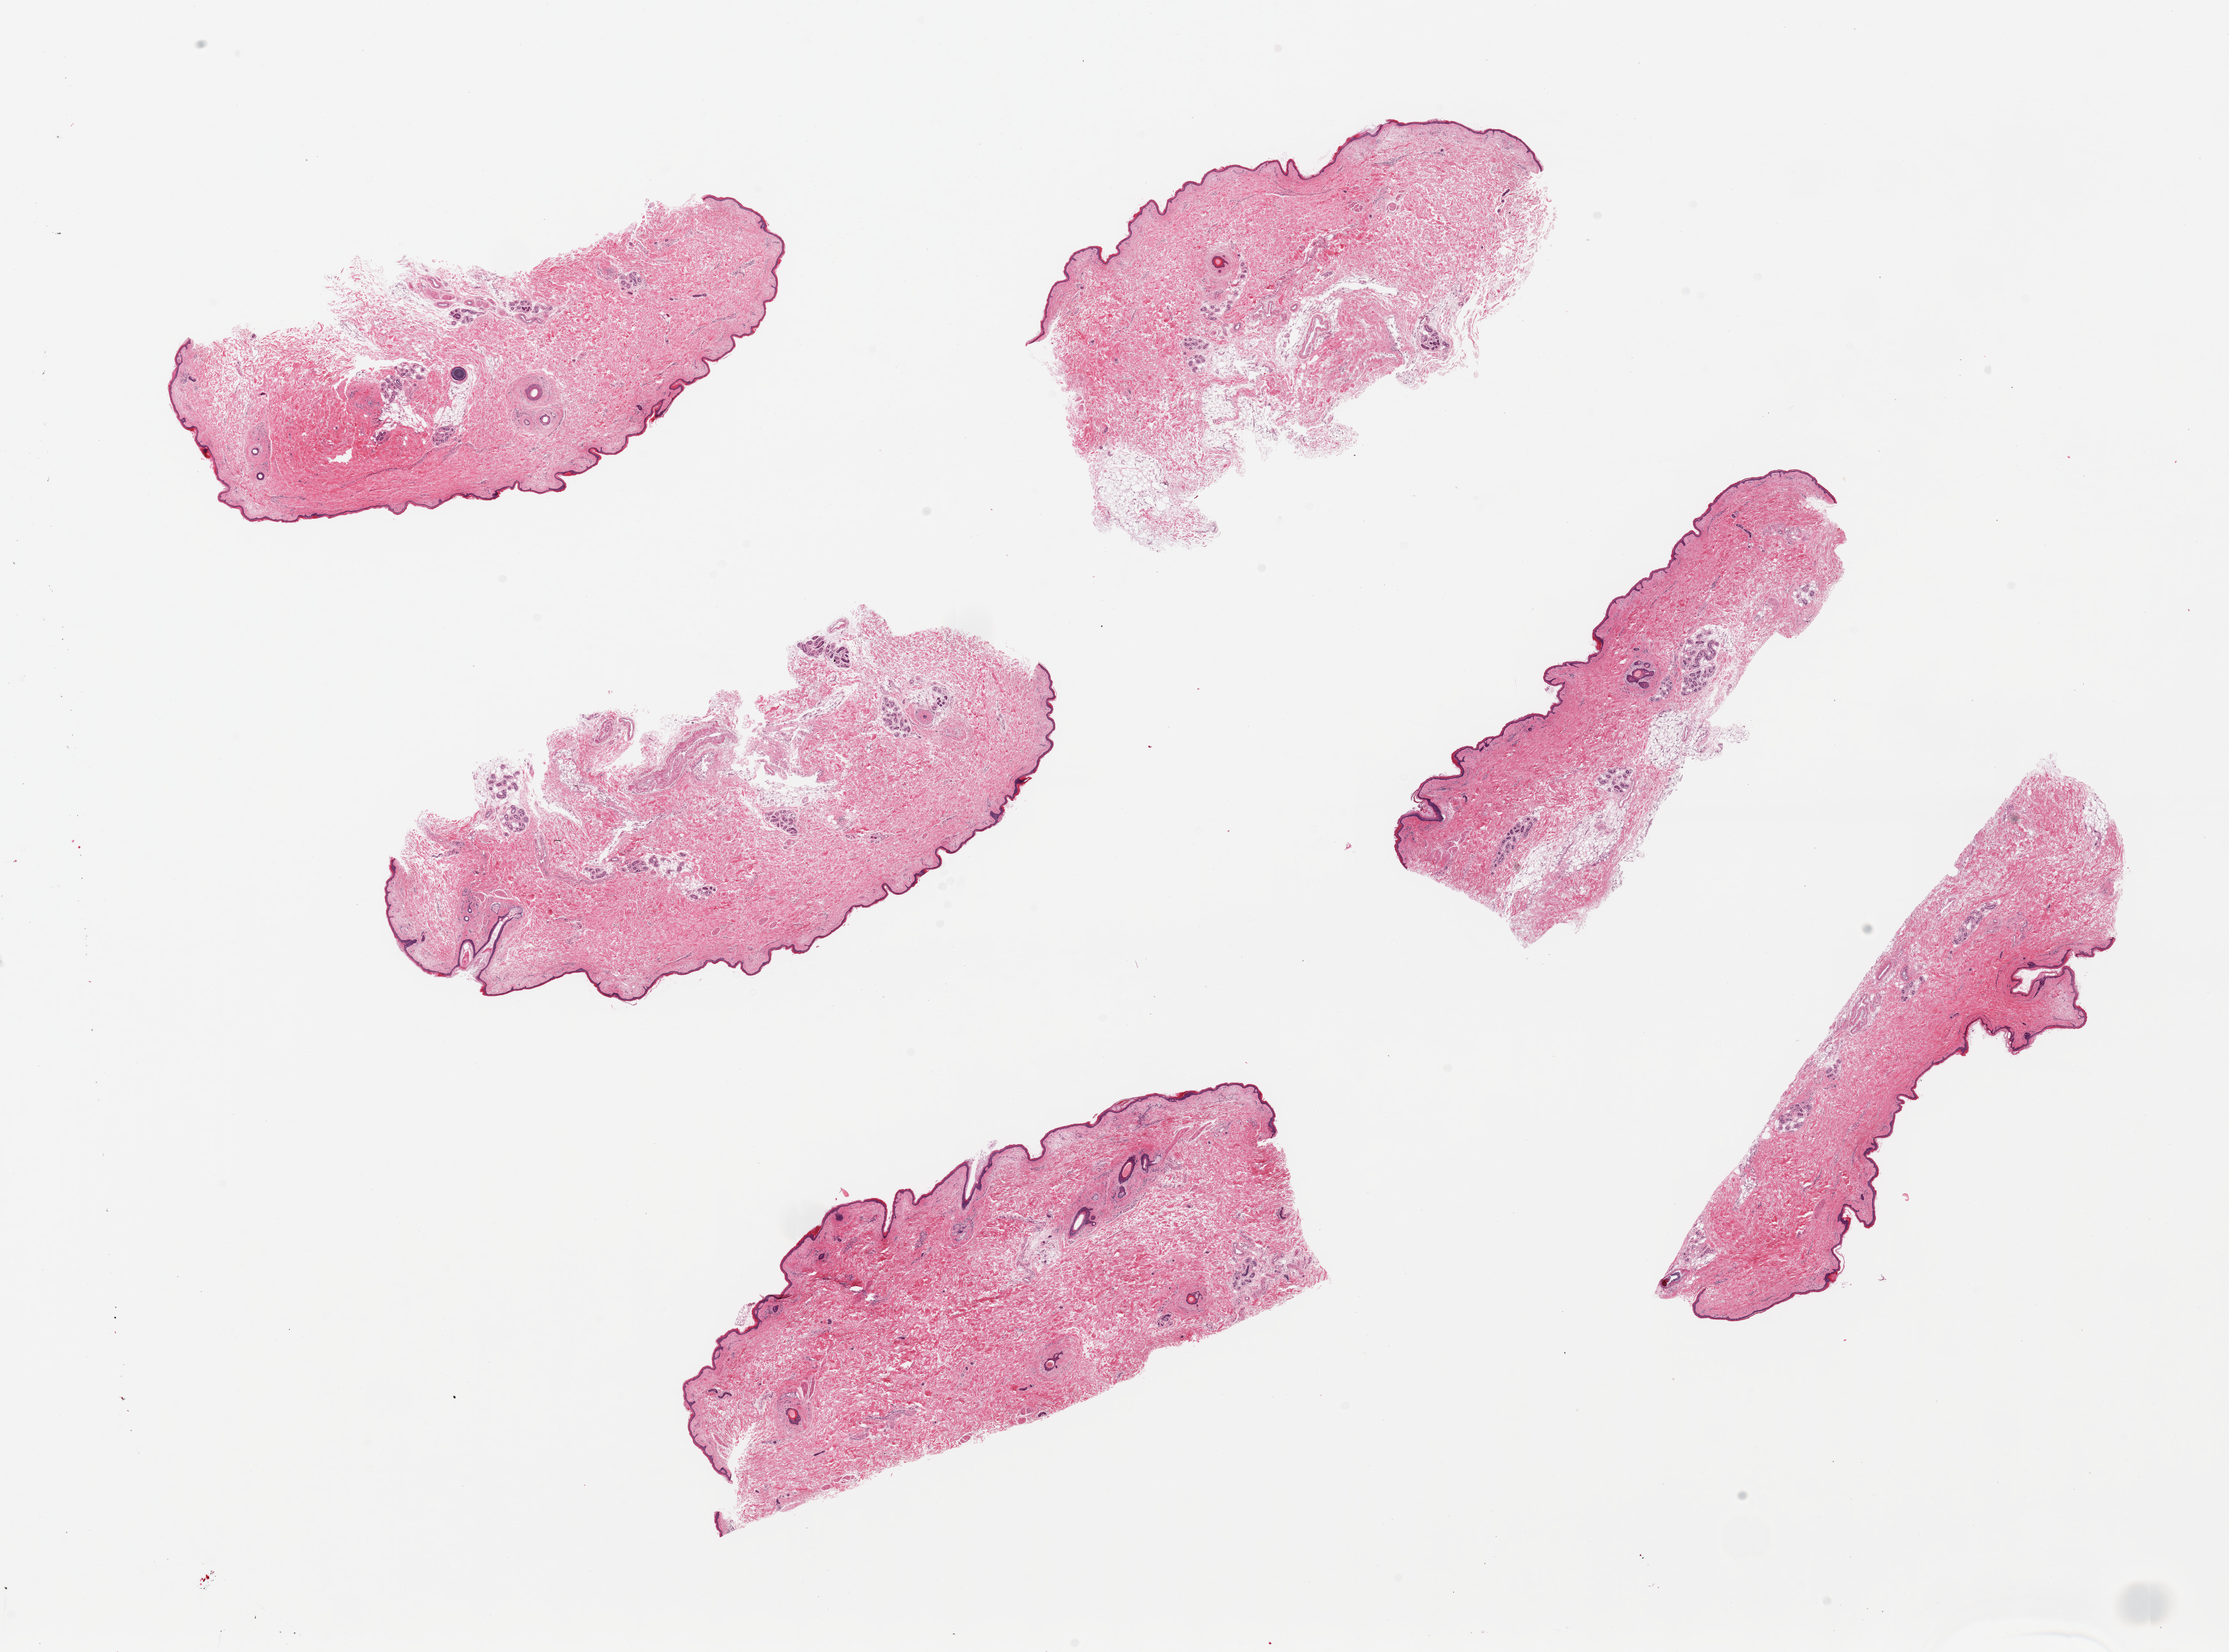
Hematoxylin and eosin (H&E) whole-slide image — a low-resolution overview of the entire scanned area, about 27.6 x 20.4 mm. PAXgene-fixed, paraffin-embedded tissue. Sampled site (target tissue): skin of suprapubic region. Tissue donor sample. Male donor.
Reviewer comment on this tissue sample: 6 pieces up to 8x4mm; squamous epithelium appears atrophic.